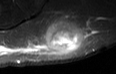
MRI of an extremity soft-tissue mass, one axial slice. Slice 24 of 36 in the series (ordered by position). STIR. MR volume resampled by the dataset authors to the PET/CT grid (not the native acquisition matrix). 3.27 mm slice thickness. 116 × 74 image matrix, field of view 113 × 72 mm. Male patient. Case-level facts recorded for this patient, not image findings: histological type: pleiomorphic leiomyosarcoma; grade: high; site of the primary tumour: left buttock.
Structures marked on this image (expert contour drawn on MRI and transferred to this co-registered scan by the dataset authors):
- gross tumour volume including surrounding oedema: box from (x=41, y=23) to (x=77, y=54) px
- gross tumour volume (mass): (x=41, y=26)–(x=76, y=54)